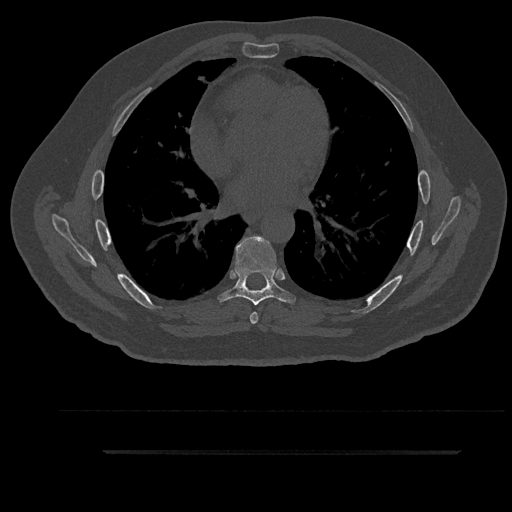
CT including the spine, one axial slice. Position 536 of 797 along the scan axis. Bone window (W 1800 / L 400 HU). 0.5 mm slice thickness. 512 × 512 image matrix, field of view 432 × 432 mm. Male patient, age 63 years. From the clinical record (not read from this slice): primary cancer: renal.
Structures marked on this image (semi-automatically segmented with operator editing):
- T6 vertebra: bounding box (x1, y1, x2, y2) in pixels: (250, 312, 258, 324)
- T7 vertebra: (218, 236, 296, 306)